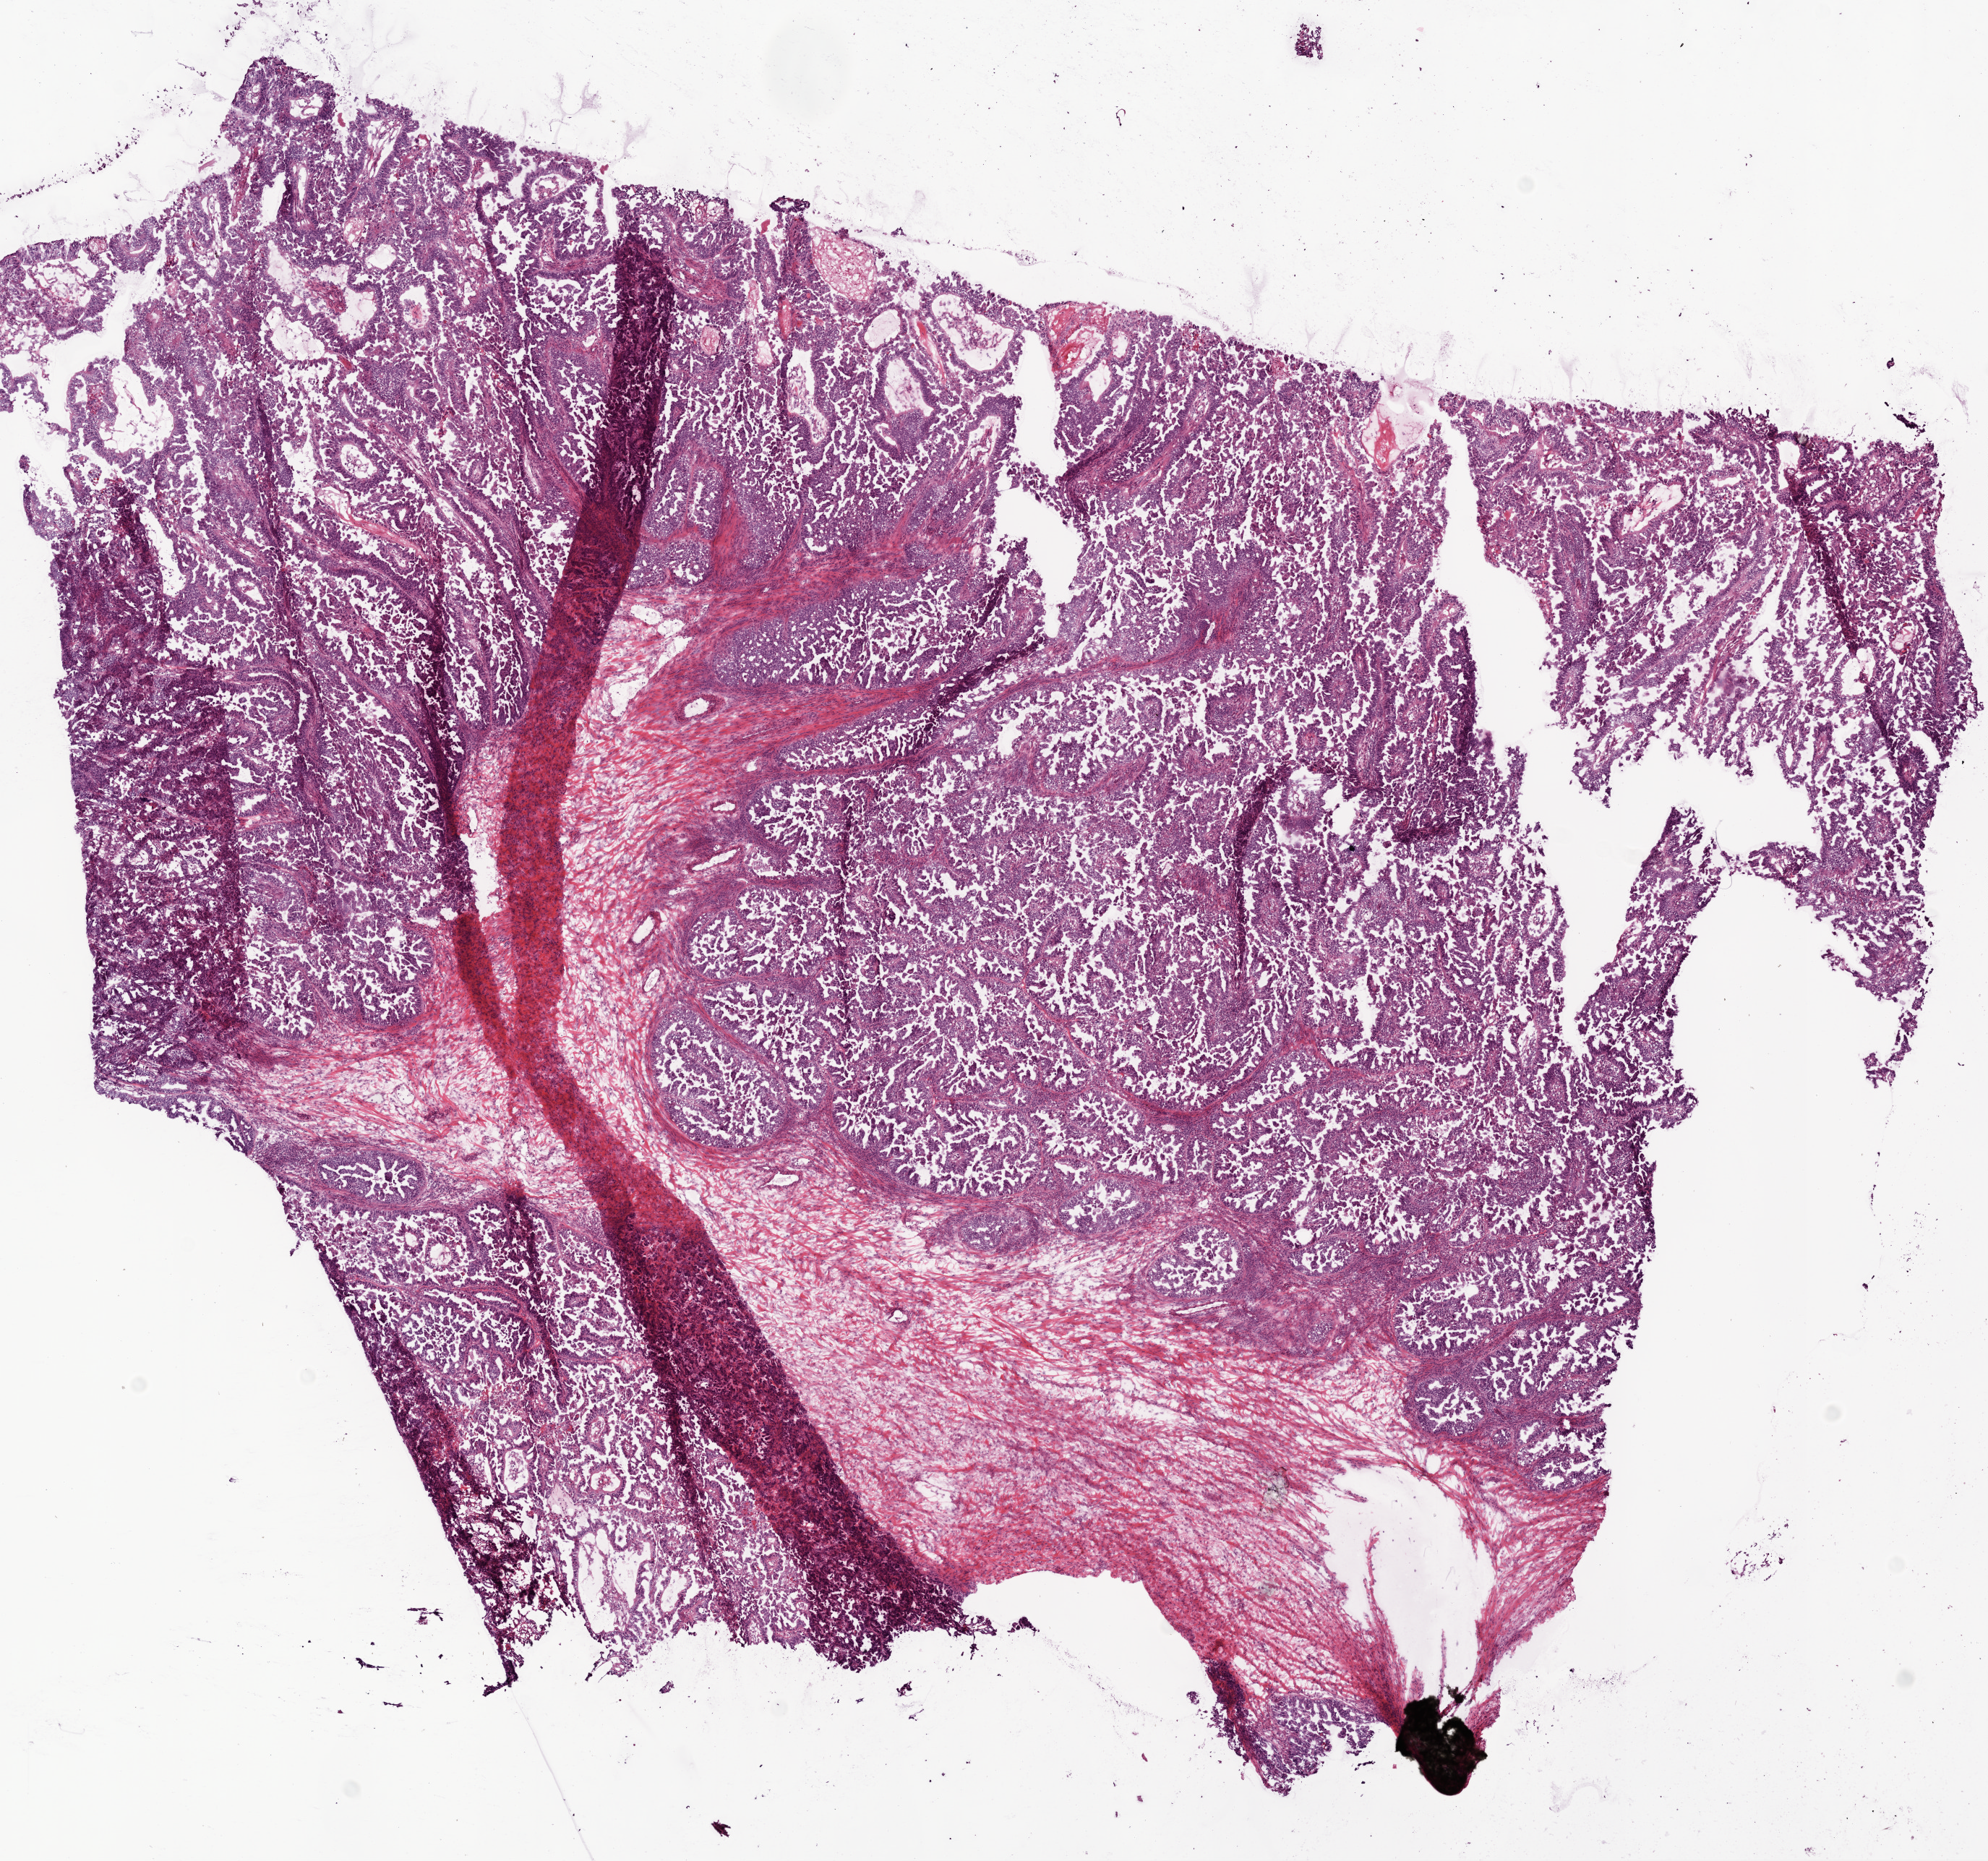
Whole-slide histology image, H&E-stained — low-resolution overview of the scanned area, about 11.0 x 10.3 mm (from a 20x scan), frozen section, ovary, primary tumour sample. Patient: female, age at initial diagnosis 53 years. Histologic grade: G2 (moderately differentiated). Slide review estimates, as recorded: tumour cells 95%, tumour nuclei 80%, normal cells 0%, stromal cells 0%, necrosis 5%. Inflammatory infiltration, as recorded: lymphocyte infiltration 10%.
FIGO stage: IIC. Pathologic diagnosis: Serous cystadenocarcinoma, NOS. Laterality: bilateral.